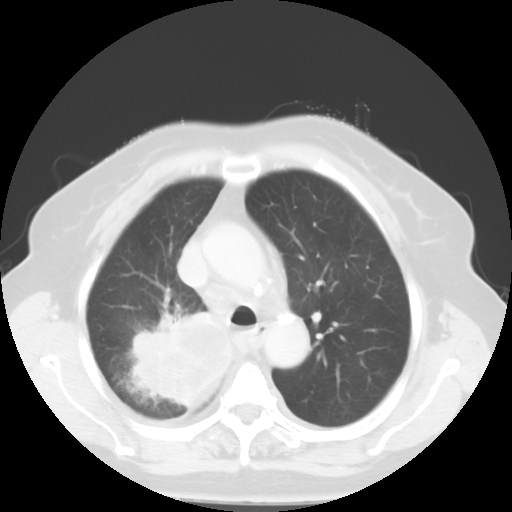
Chest CT, one axial slice. Reconstruction kernel STANDARD. Lung window (W 1500 / L -600 HU). 512 × 512 image matrix. Patient: female, 81 years. Case-level facts recorded for this patient, not image findings: clinical TNM (as recorded): T4 N3 M1b.
Structures marked on this image (rectangle marked by the reading radiologist):
- lung tumour (recorded histology: adenocarcinoma): bounding box (x1, y1, x2, y2) in pixels: (128, 308, 238, 409)